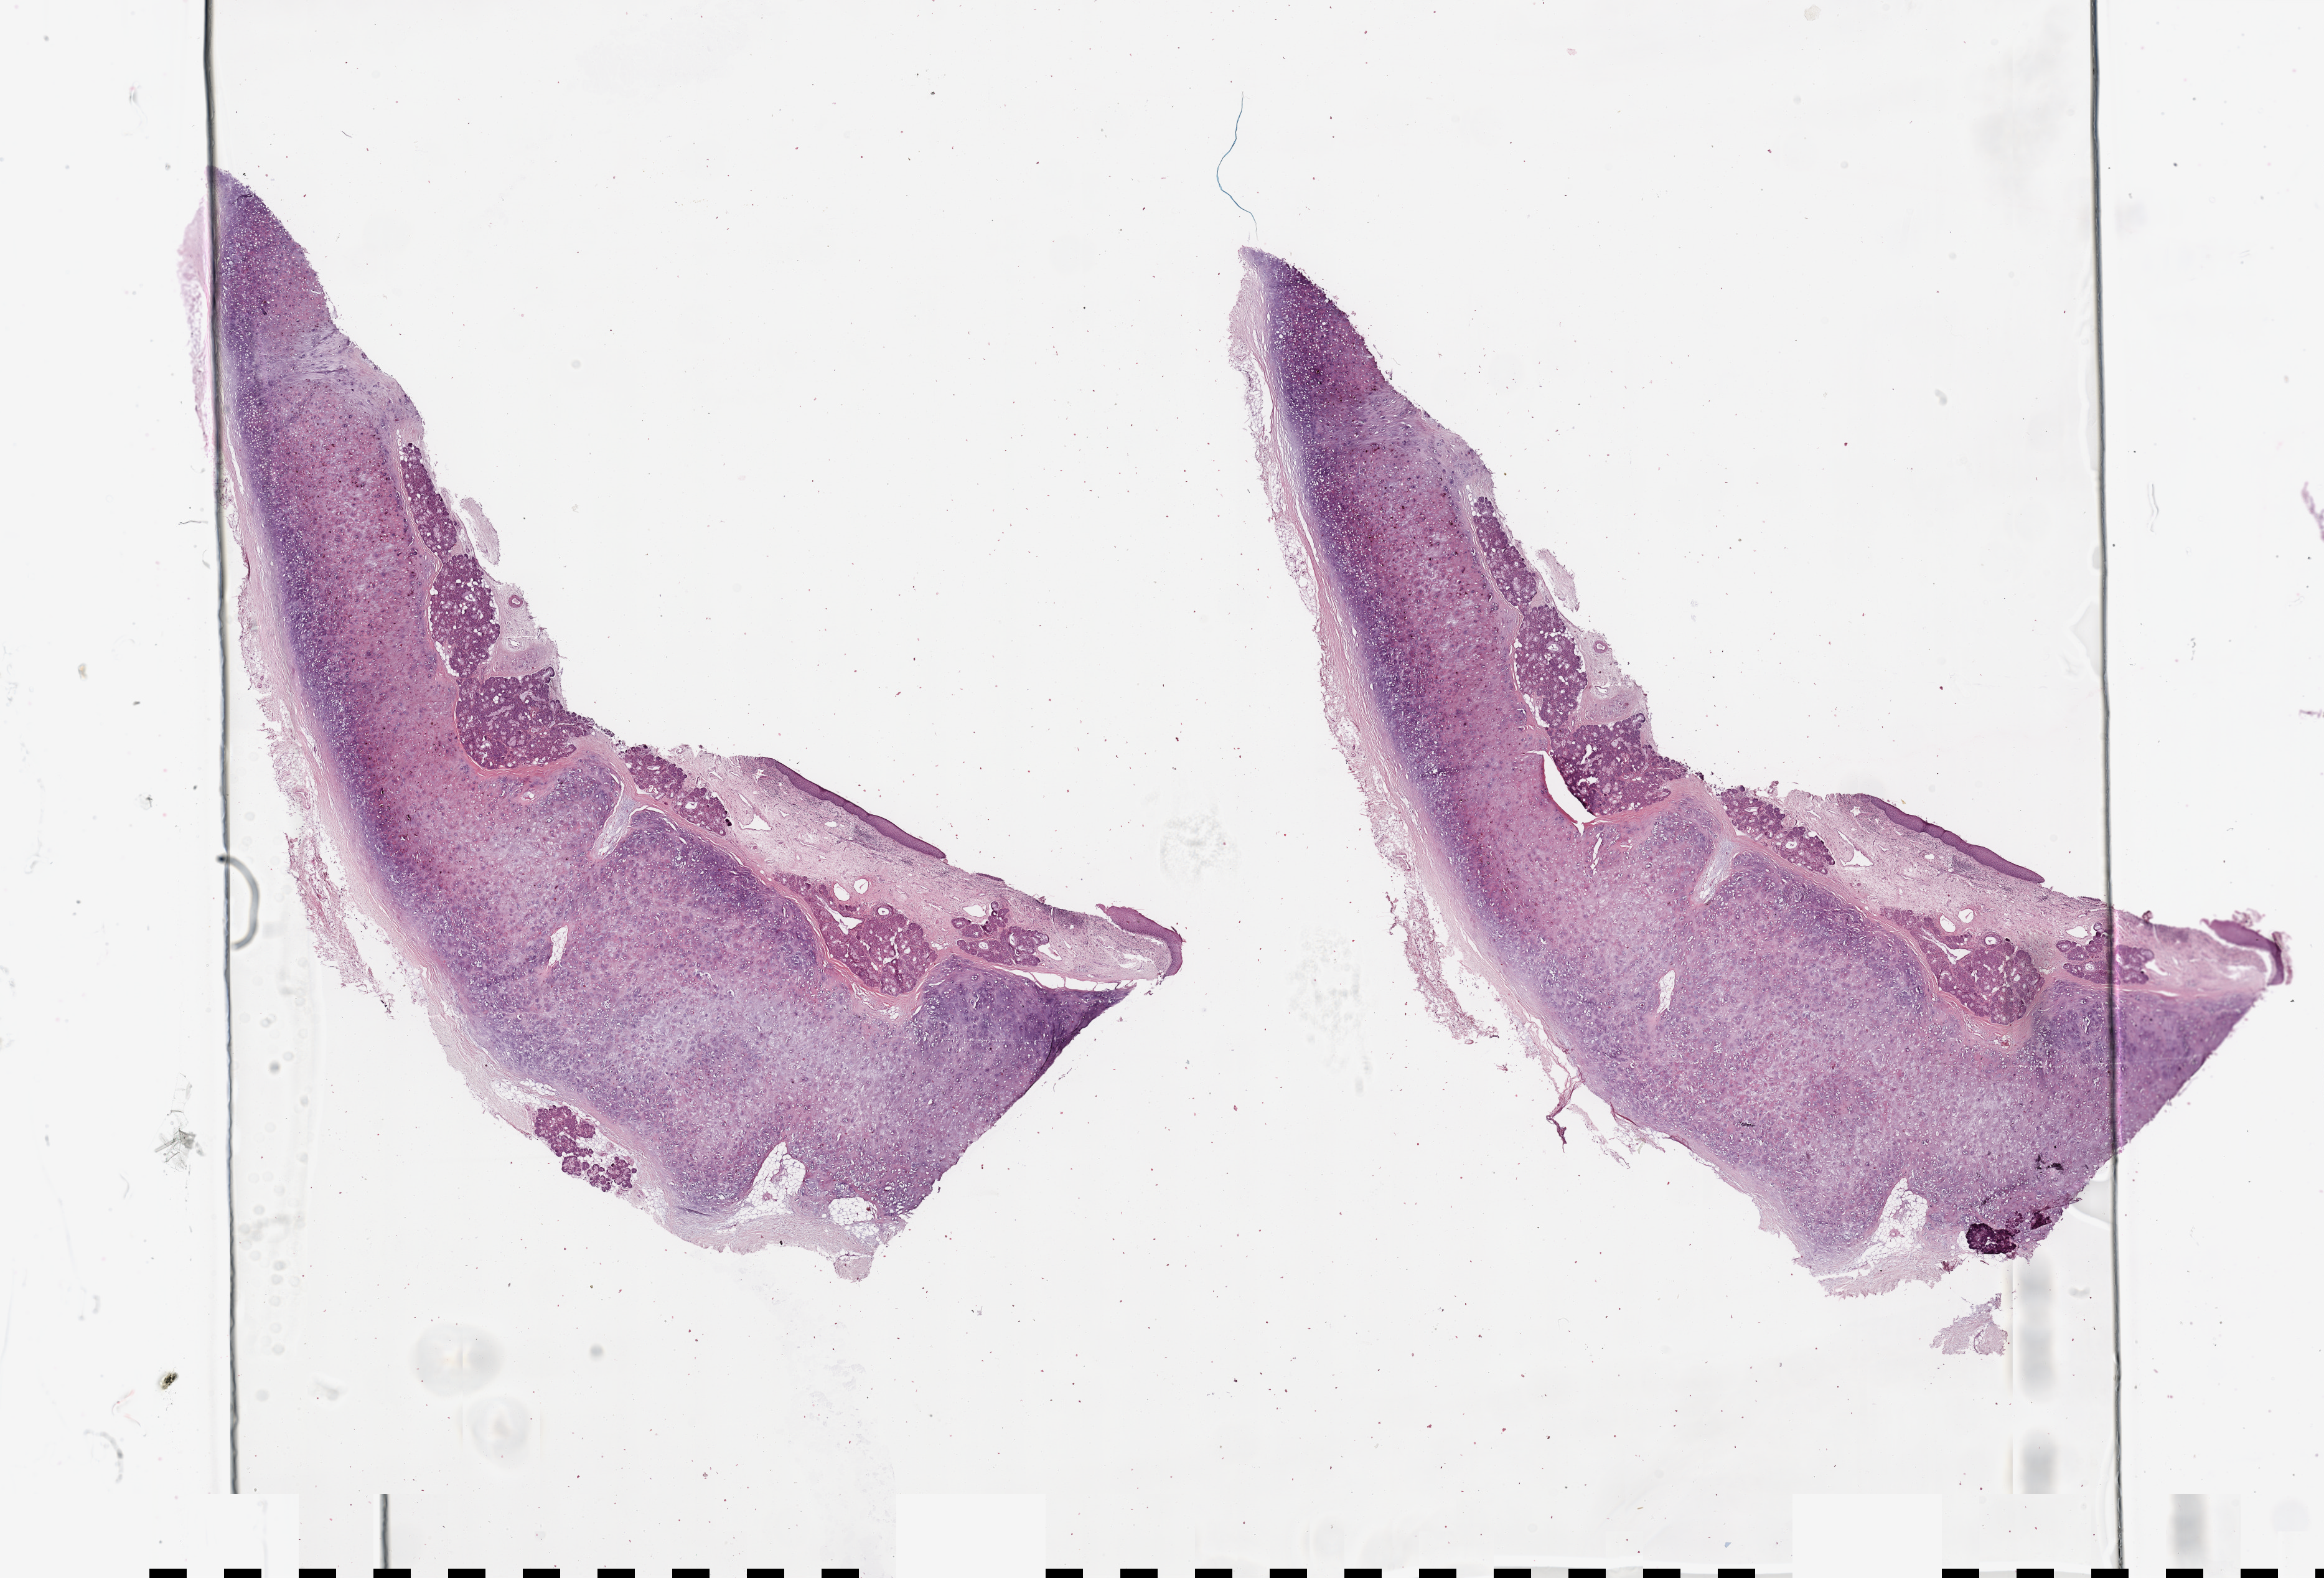
Digitized H&E tissue section (whole slide), low-resolution overview of the scanned area, about 29.5 x 20.0 mm (from a 20x scan), normal (non-tumour) tissue sample, sampled site: larynx. 64-year-old male patient.
This section: normal (non-tumour) tissue from the same patient. Patient diagnosis: Squamous cell carcinoma, NOS (larynx, NOS).